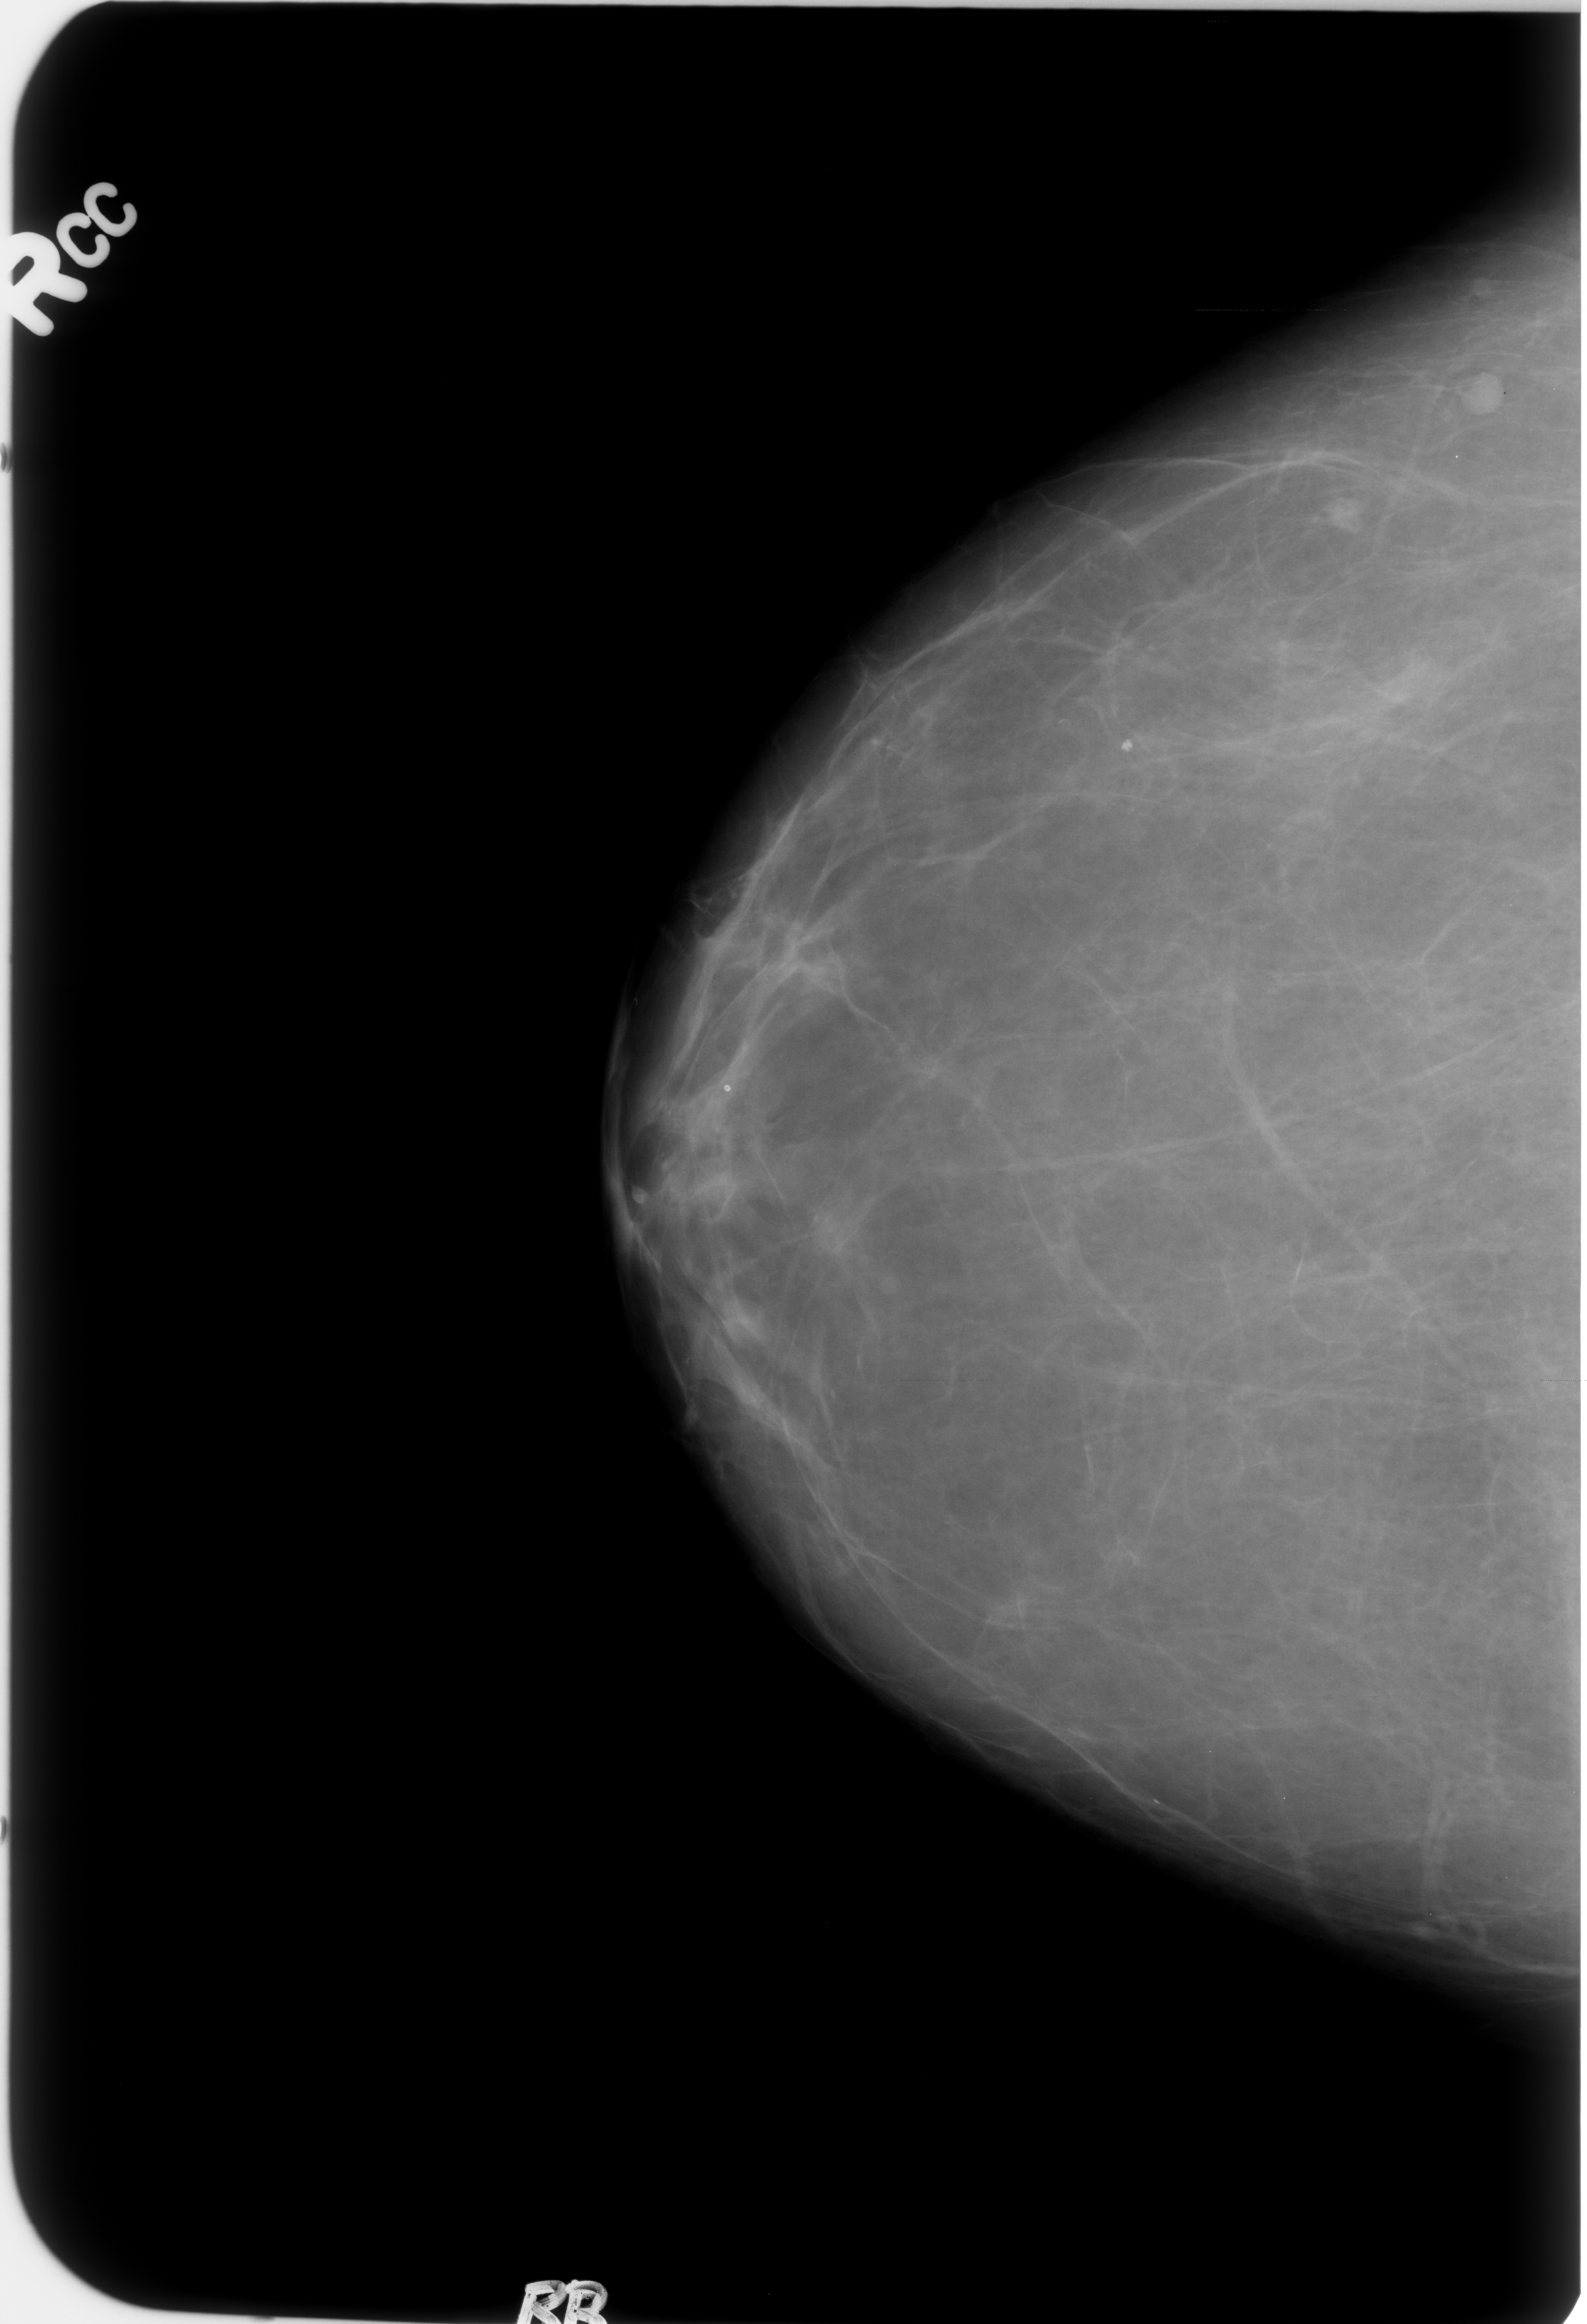
Mammogram (digitized film), right breast, craniocaudal (CC) view, BI-RADS breast density category 1 (scale 1–4).
Calcifications, morphology coarse; BI-RADS assessment category 2; subtlety rating 4 on a 1 (subtle) to 5 (obvious) scale; benign without callback (not worked up further).